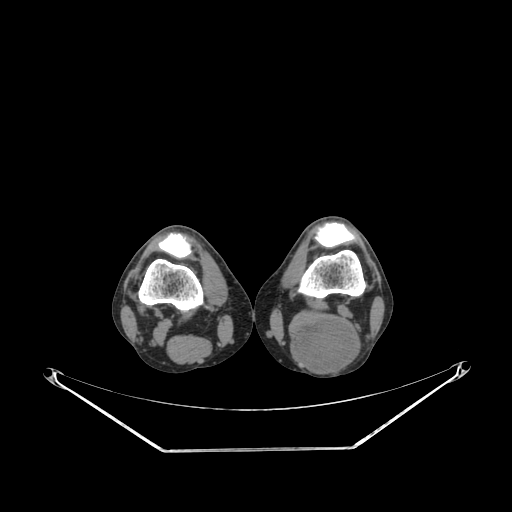
CT of an extremity soft-tissue mass (from a PET/CT study), one axial slice. Slice 186 of 267 in the series (ordered by position). Soft-tissue window (W 400 / L 40 HU). 3.75 mm slice thickness. 512 × 512 image matrix. Male patient. From the clinical record (not read from this slice): histological type: synovial sarcoma; site of the primary tumour: left poplietal fossa.
Outlined on this slice (expert contour drawn on MRI and transferred to this co-registered scan by the dataset authors):
- gross tumour volume (mass): bounding box (x1, y1, x2, y2) in pixels: (290, 315, 362, 373)